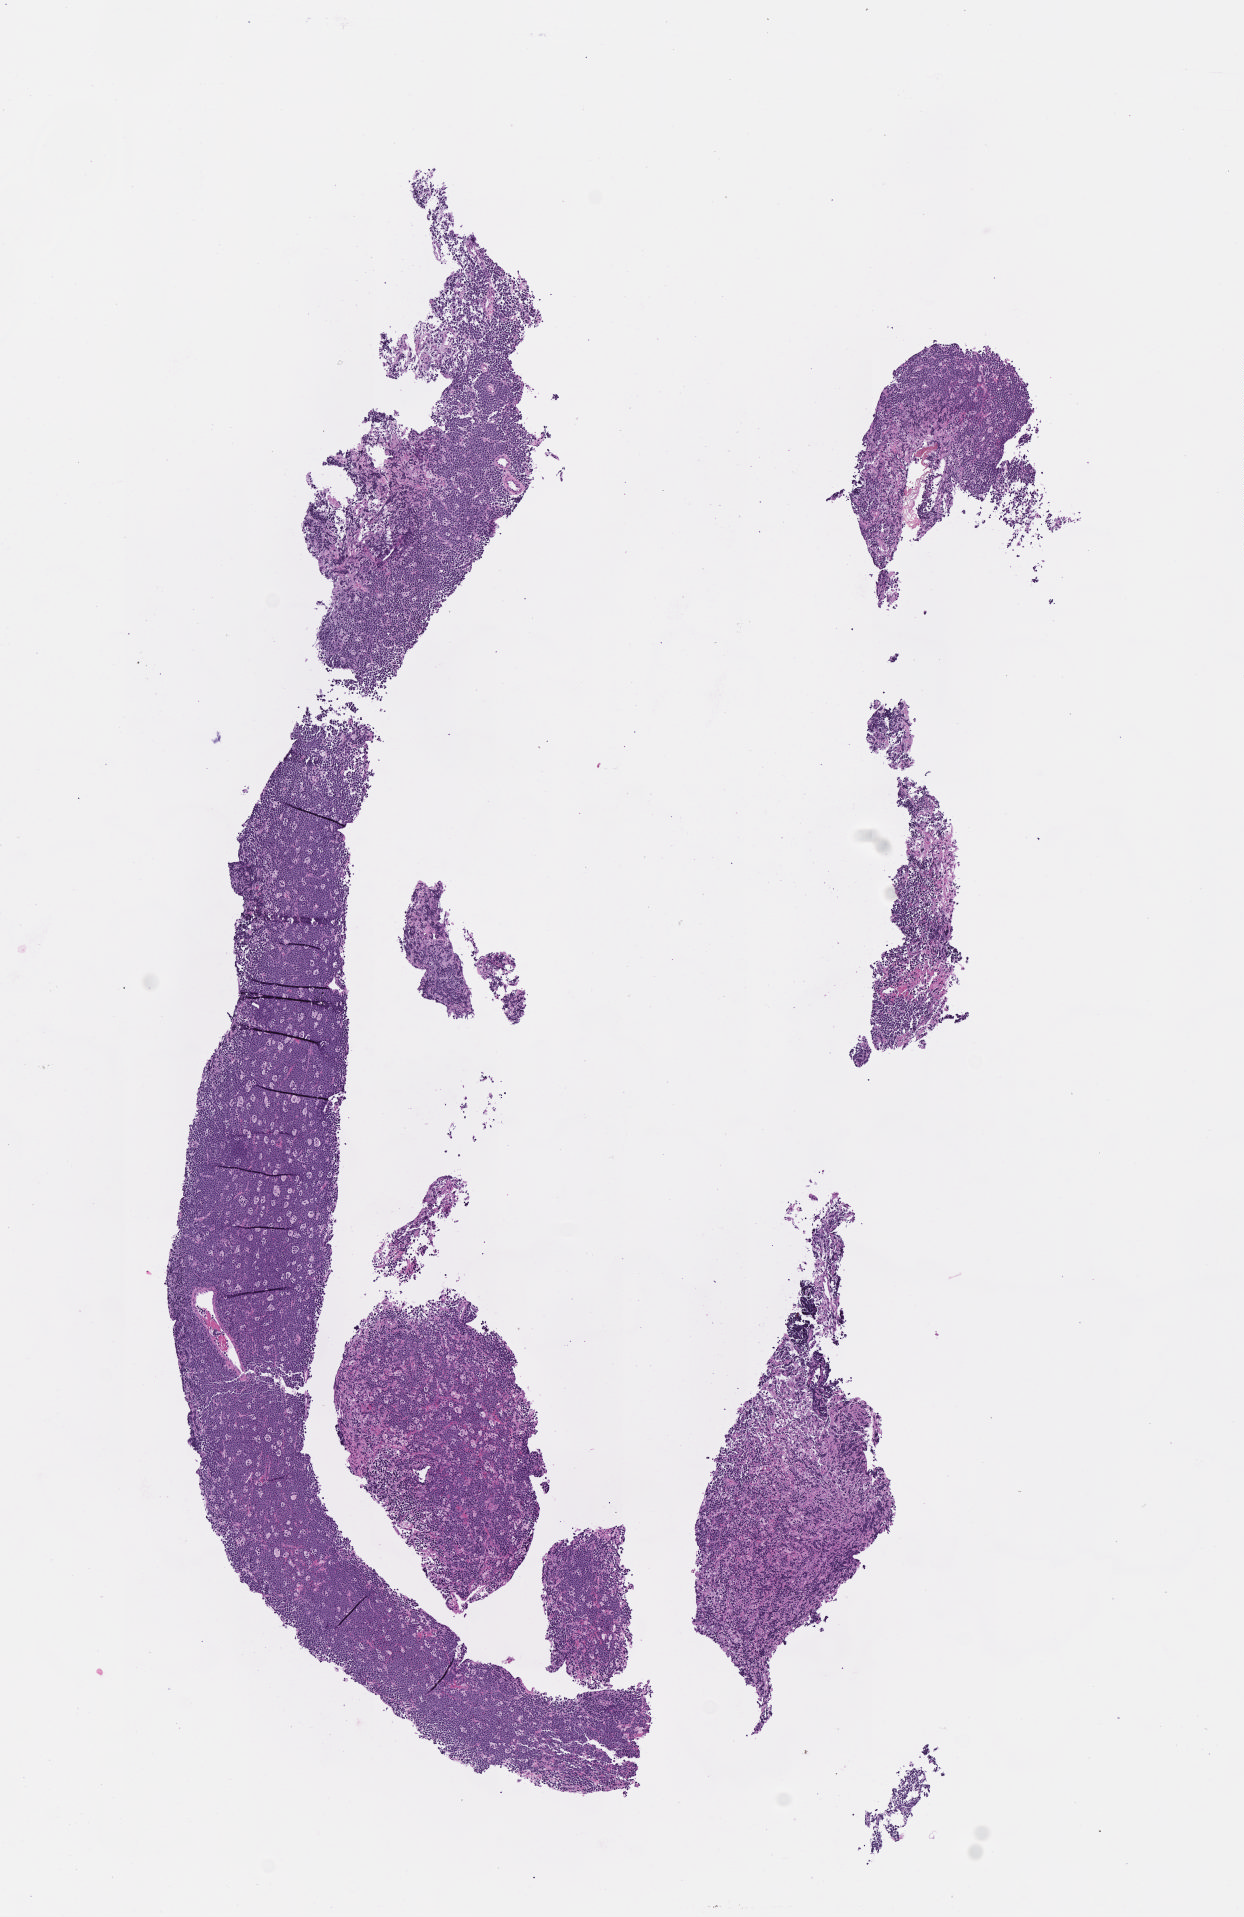
H&E whole-slide image — a low-resolution overview of the entire scanned area, about 5.0 x 7.8 mm, formalin-fixed, paraffin-embedded (FFPE) tissue, specimen: primary tumor. Patient: female, 10 years old. Composition of this section per pathologist review: tumor cells 95%, tumor nuclei 95%, stromal cells 0%, necrosis 5%, normal cells 0%. Inflammatory infiltration, as recorded: lymphocyte infiltration 10%, monocyte infiltration 30%, neutrophil infiltration 10%.
Diagnosis: Burkitt lymphoma, NOS. Ann Arbor stage (patient): Stage III.